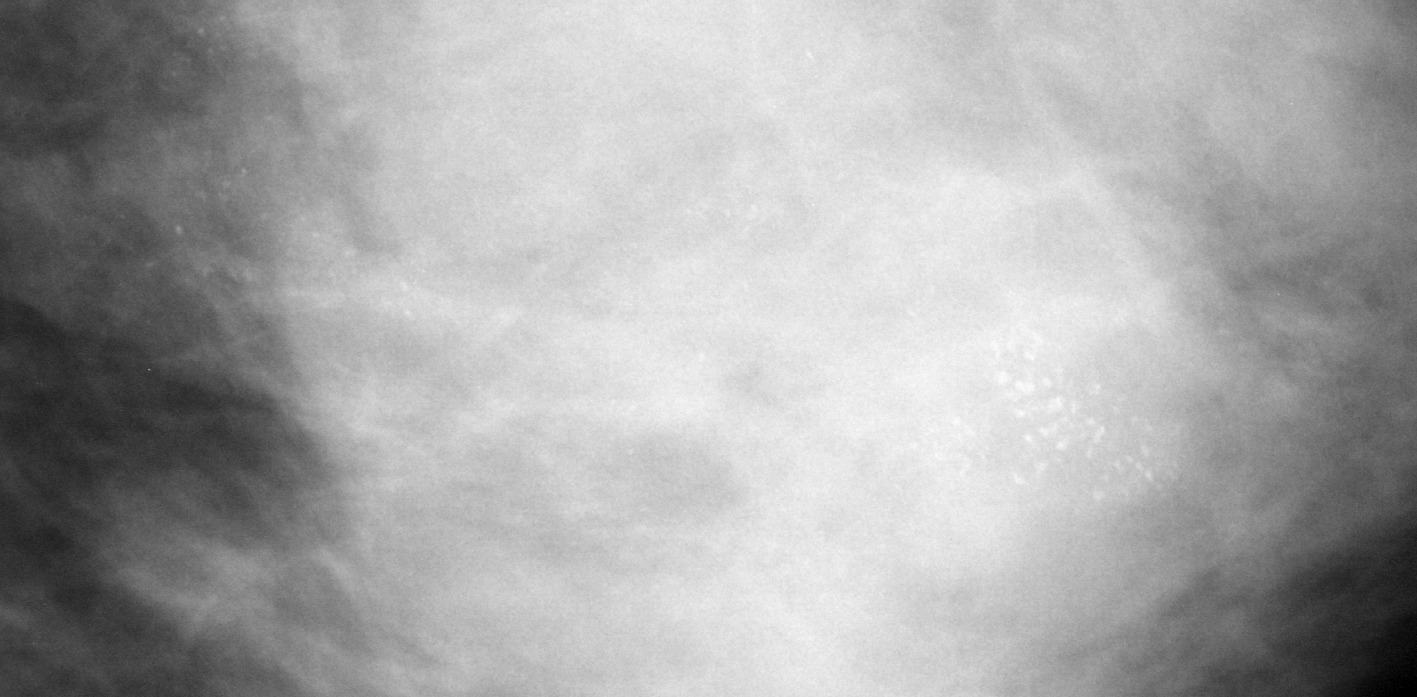
Crop from a digitized film mammogram around one marked abnormality; left breast; MLO view.
- Finding: calcifications, morphology amorphous / pleomorphic, distribution segmental; BI-RADS assessment category 5; subtlety rating 5 on a 1 (subtle) to 5 (obvious) scale; pathology result (as recorded, not read from the image): malignant.